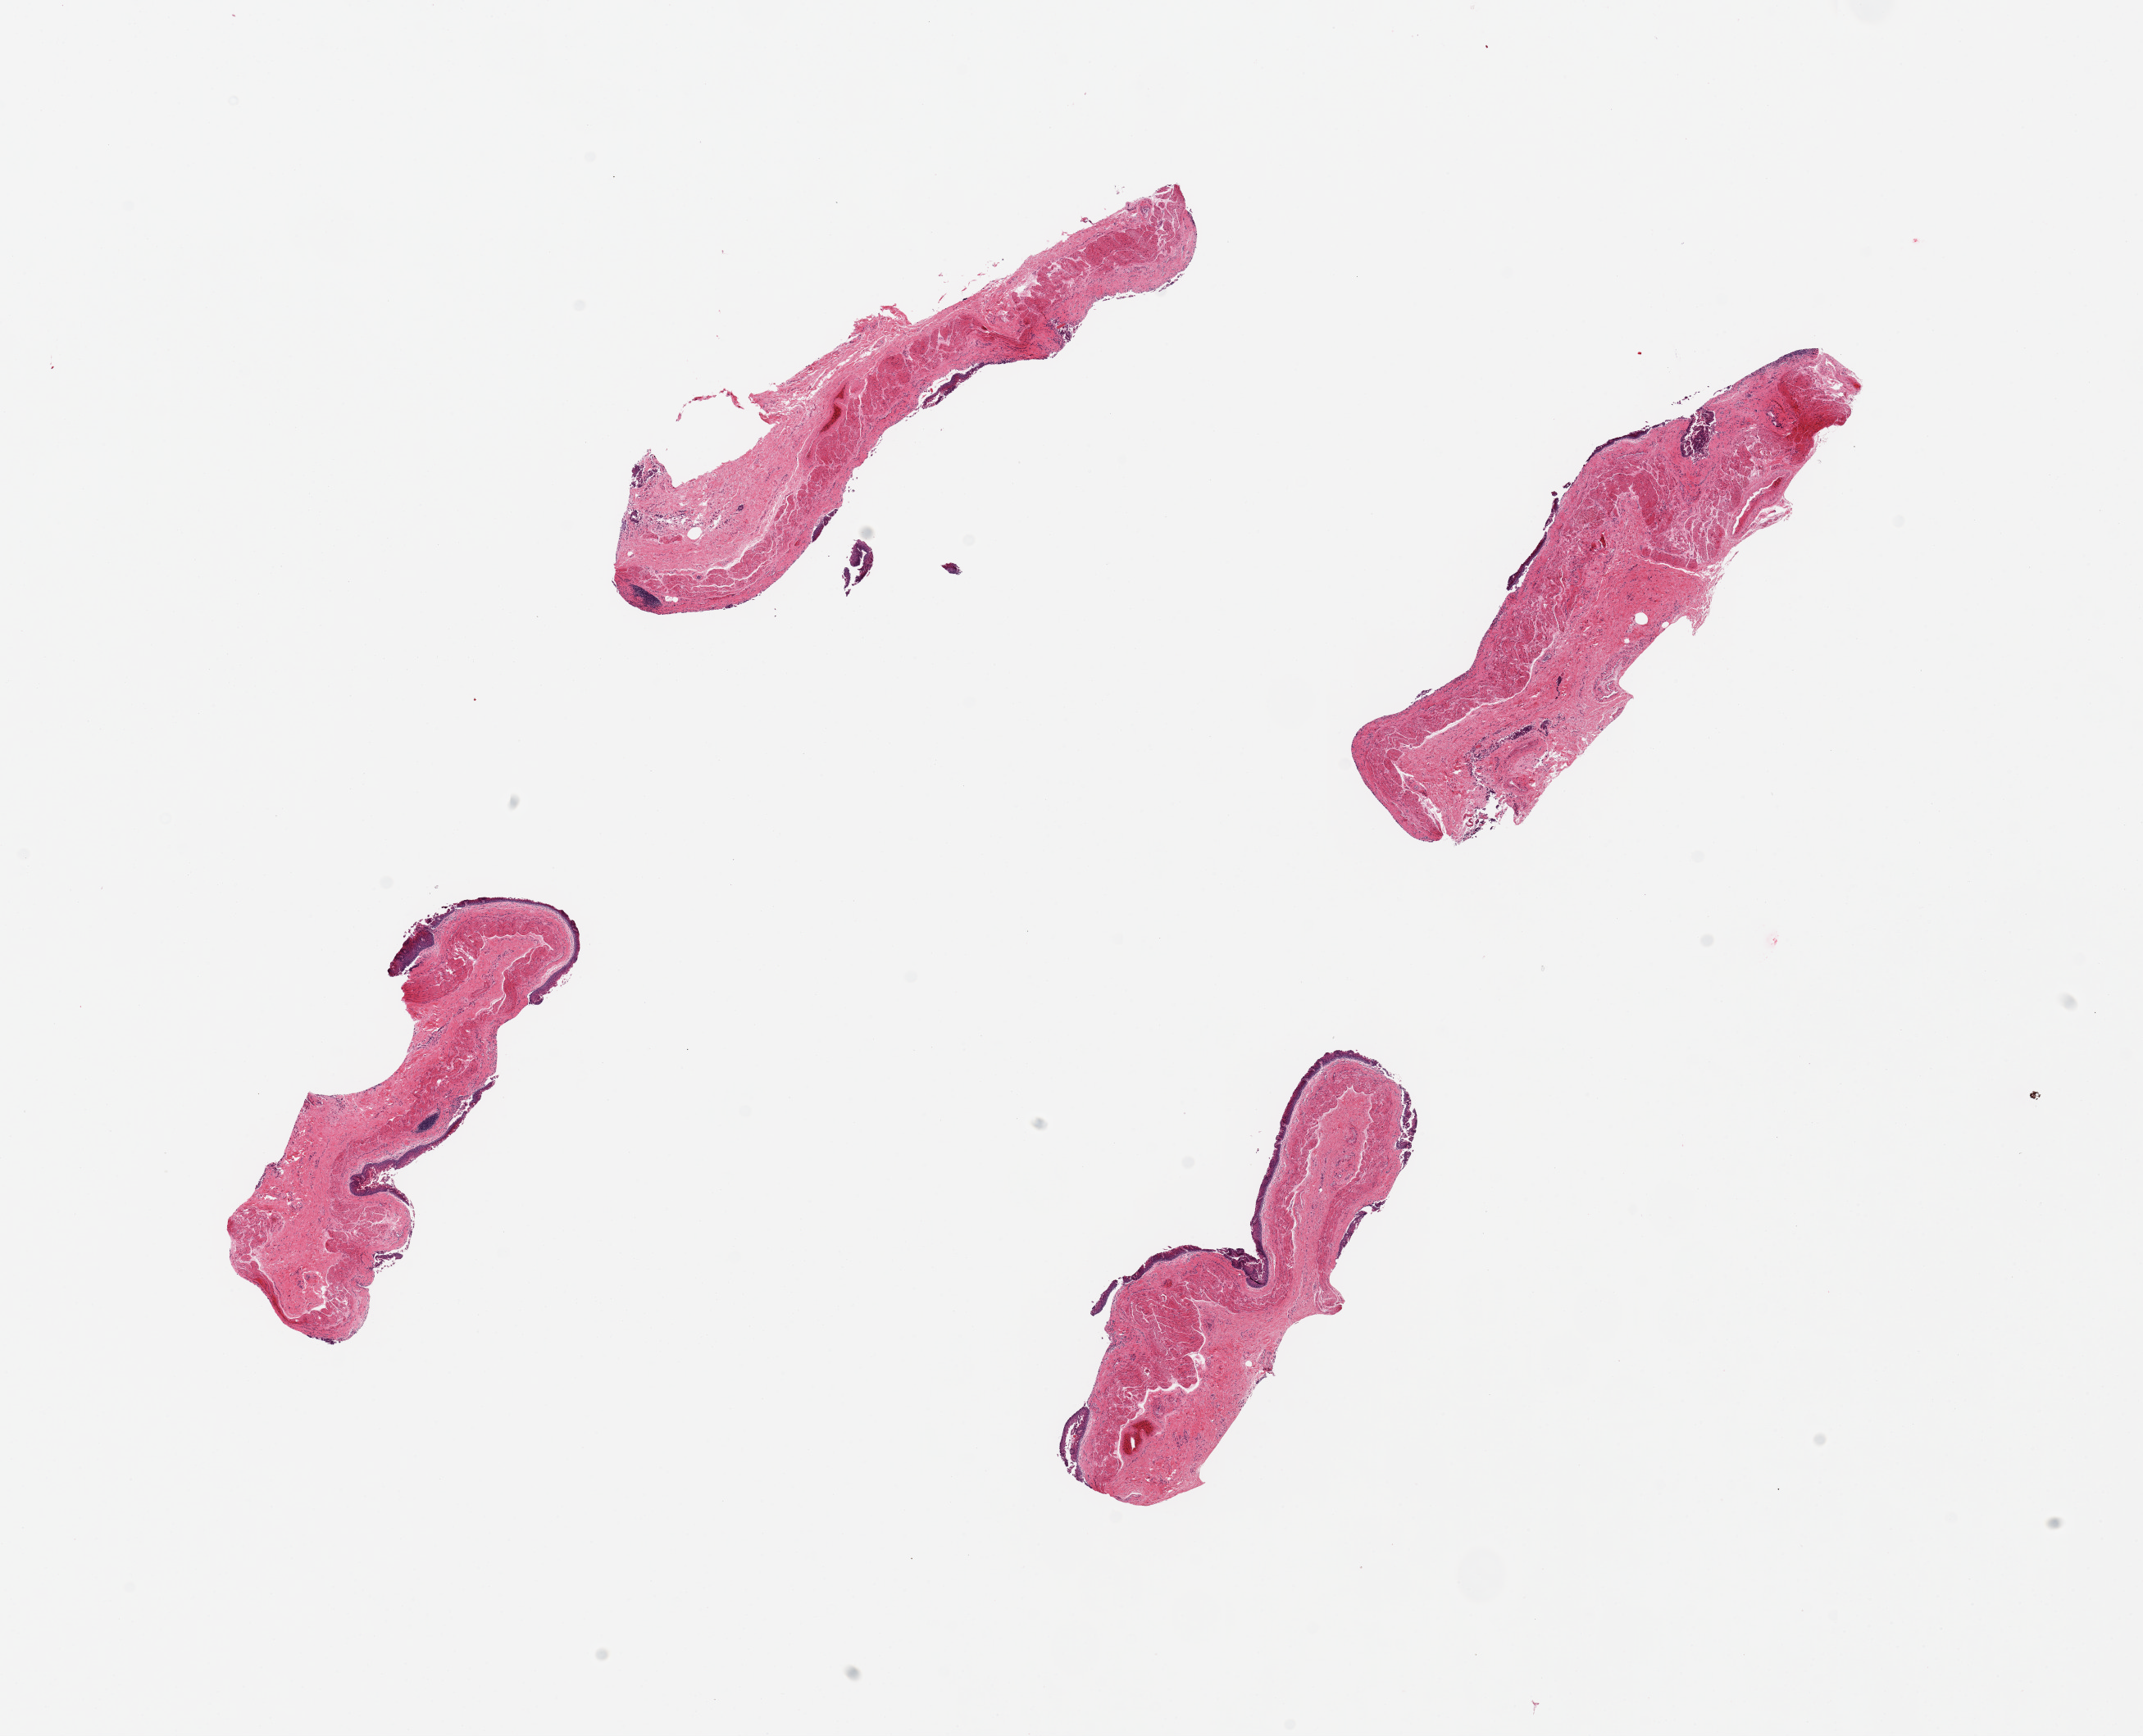
Digitized hematoxylin and eosin (H&E)-stained section, a low-resolution overview of the entire scanned area, about 20.7 x 16.8 mm. PAXgene-fixed, paraffin-embedded tissue. Section of esophageal mucous membrane (target tissue). Donor tissue sample. Female donor.
- pathologist's review note for this sample: 4 pieces; epithelium largely sloughed